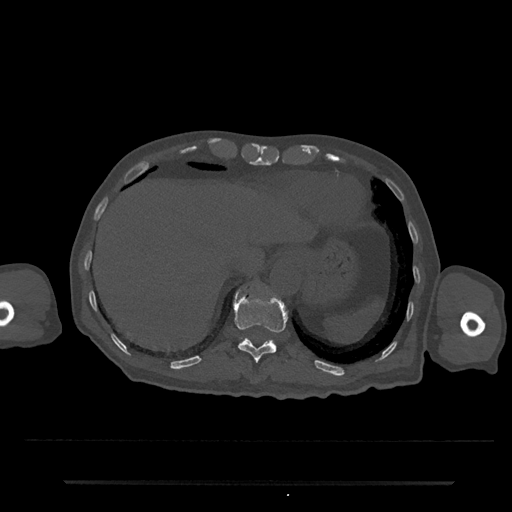
CT including the spine, one axial slice; position 249 of 797 along the scan axis; reconstruction kernel Br40s/3; bone window (W 1800 / L 400 HU); 512 × 512 image matrix, field of view 427 × 427 mm. Patient: male, 74 years. Case-level facts recorded for this patient, not image findings: primary cancer: prostate.
Annotated regions visible in this slice (semi-automatic segmentation, software-assisted and operator-edited):
- T10 vertebra: box from (x=250, y=379) to (x=259, y=384) px
- T11 vertebra: (x=233, y=289)–(x=287, y=362)